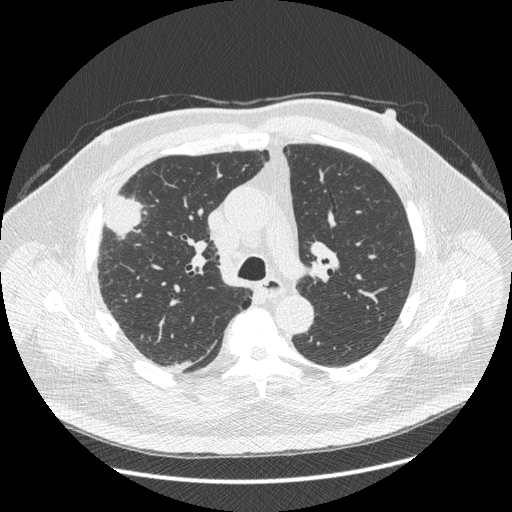
Low-dose screening chest CT, one axial slice. Slice 283 of 426 in the series (ordered by position). Reconstruction kernel STANDARD. 120 kVp. Lung window (W 1500 / L -600 HU). 1.25 mm slice thickness. 512 × 512 image matrix.
Structures marked on this image (outlined manually by an expert reader):
- lesion 1 (tumor, upper lobe of right lung): bounding box [x1, y1, x2, y2] px = [106, 195, 142, 236]